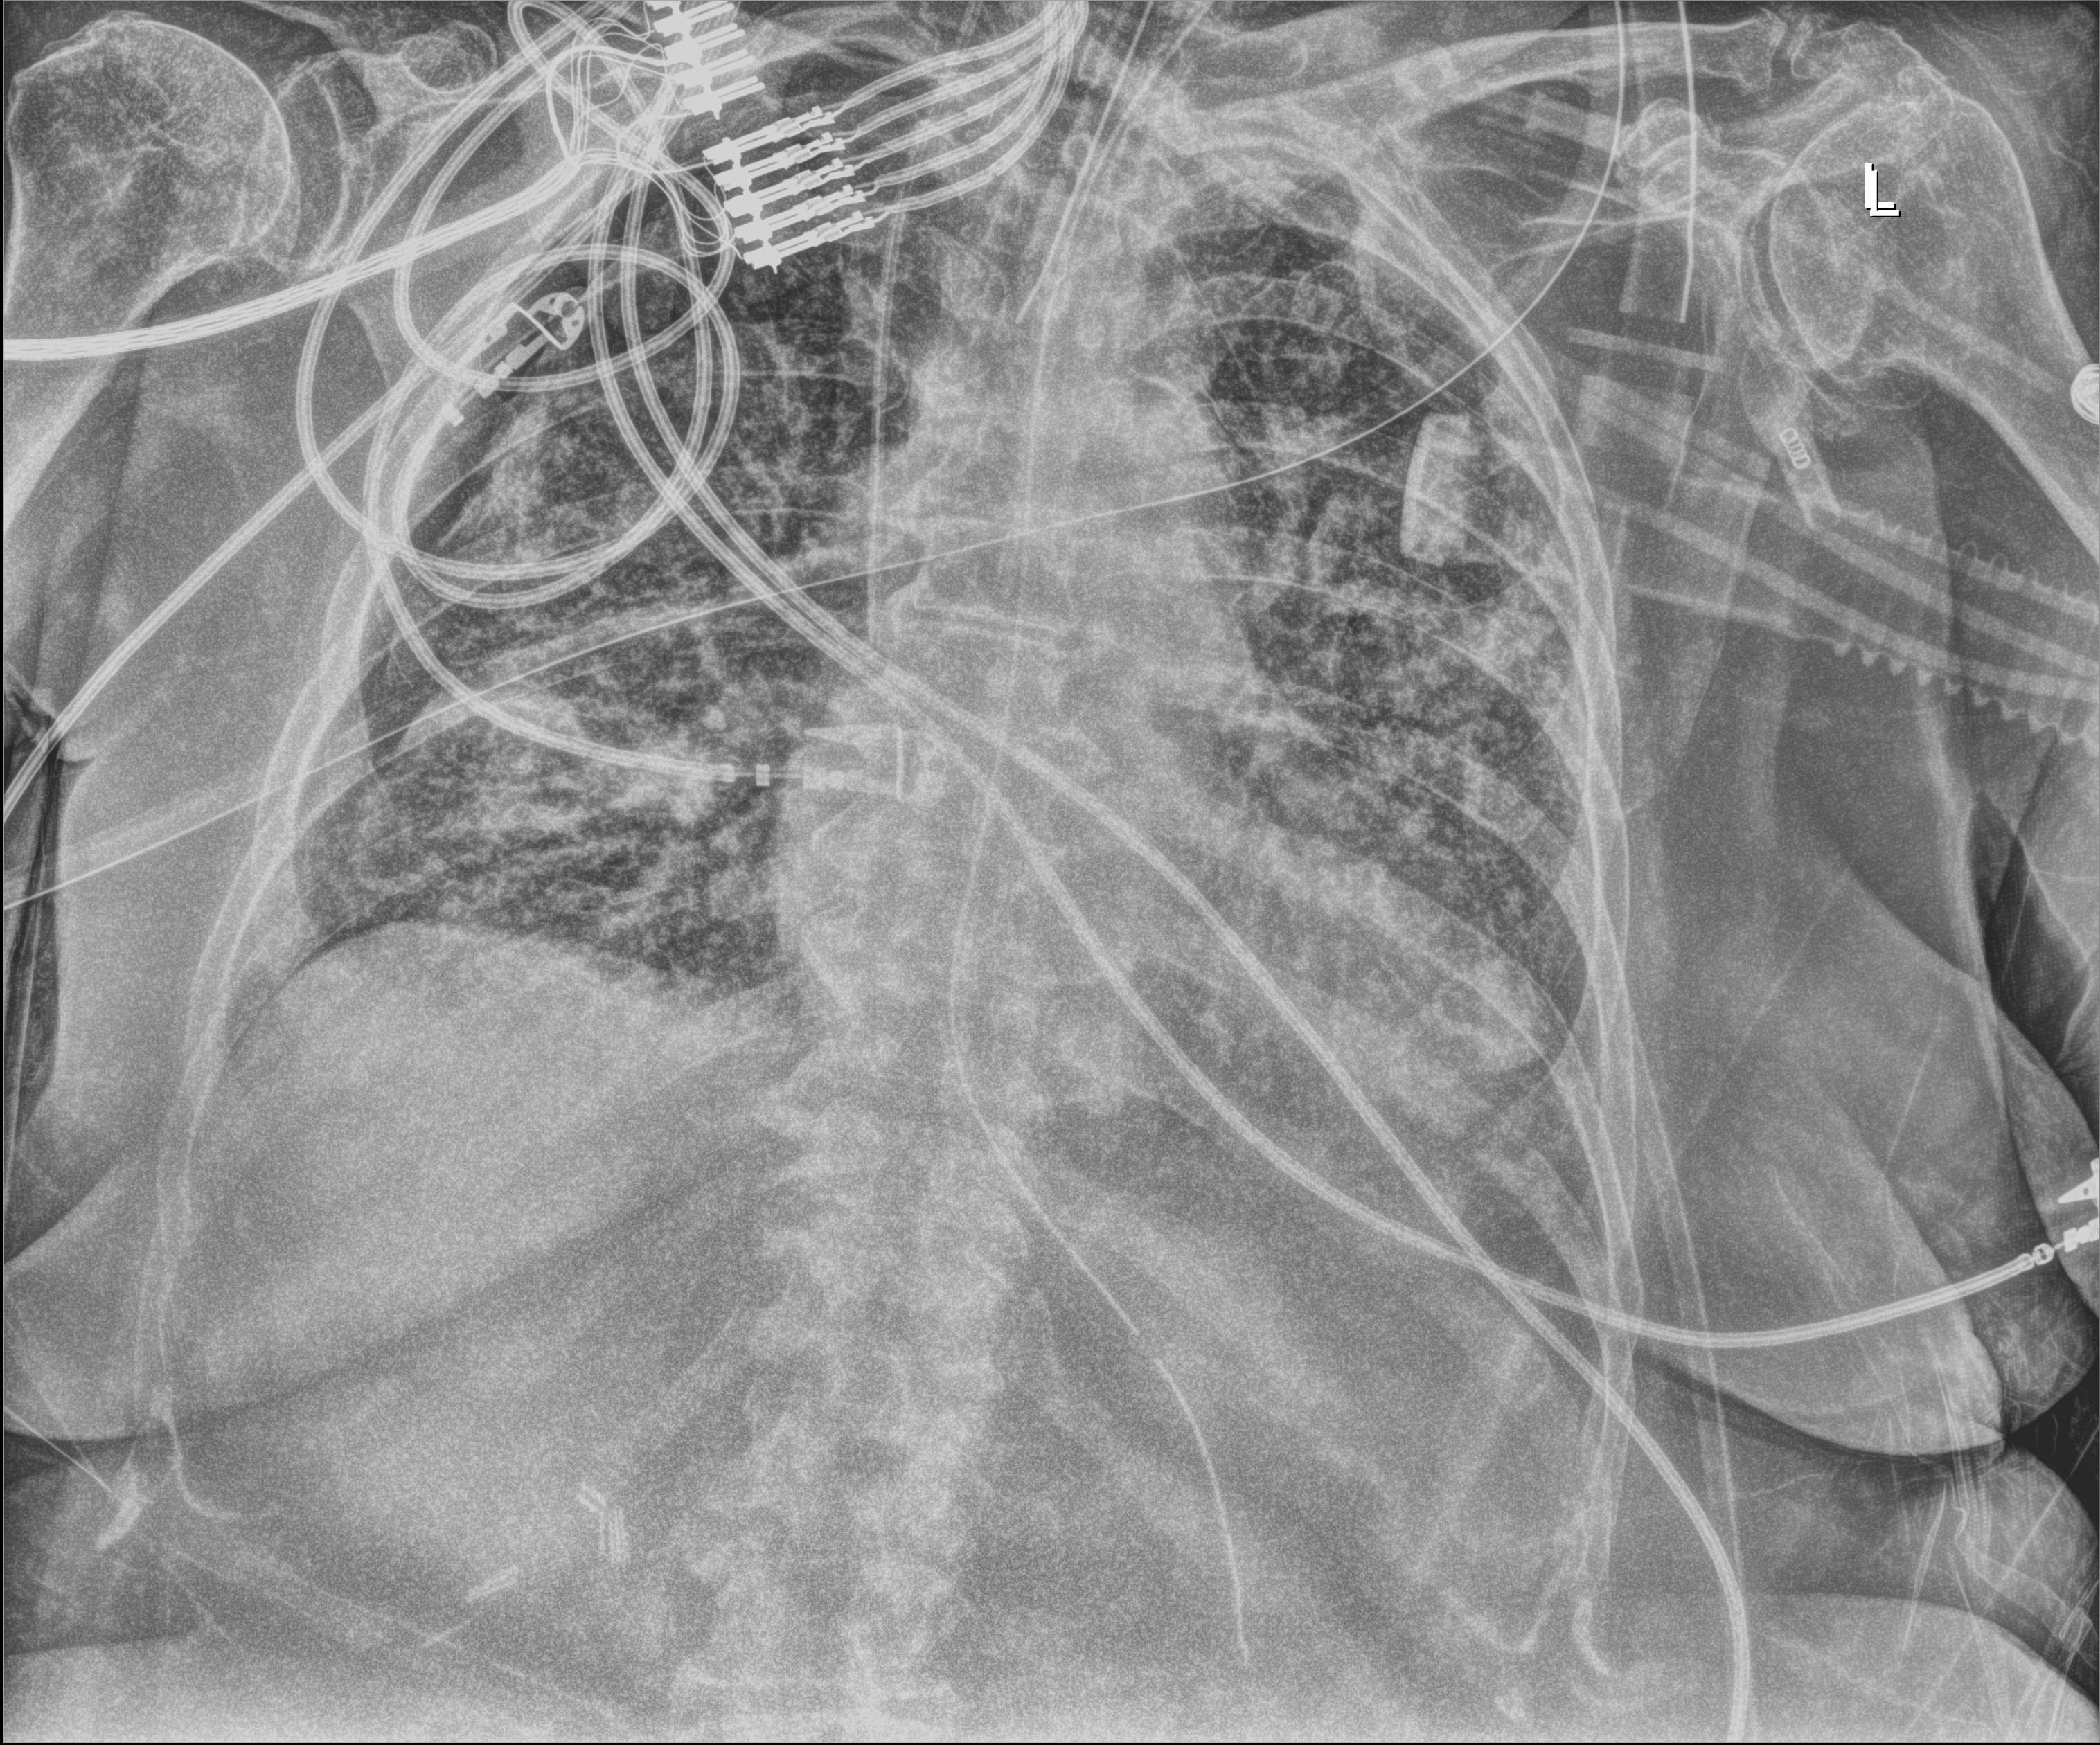
Portable chest radiograph; anteroposterior (AP) projection. Patient hospitalised with COVID-19; female, aged 75–90 years.
Hospital-stay facts (about this admission, not read from this image; timing relative to this image not recorded):
- mechanically ventilated during this hospital stay: yes
- admitted to intensive care during this hospital stay: no